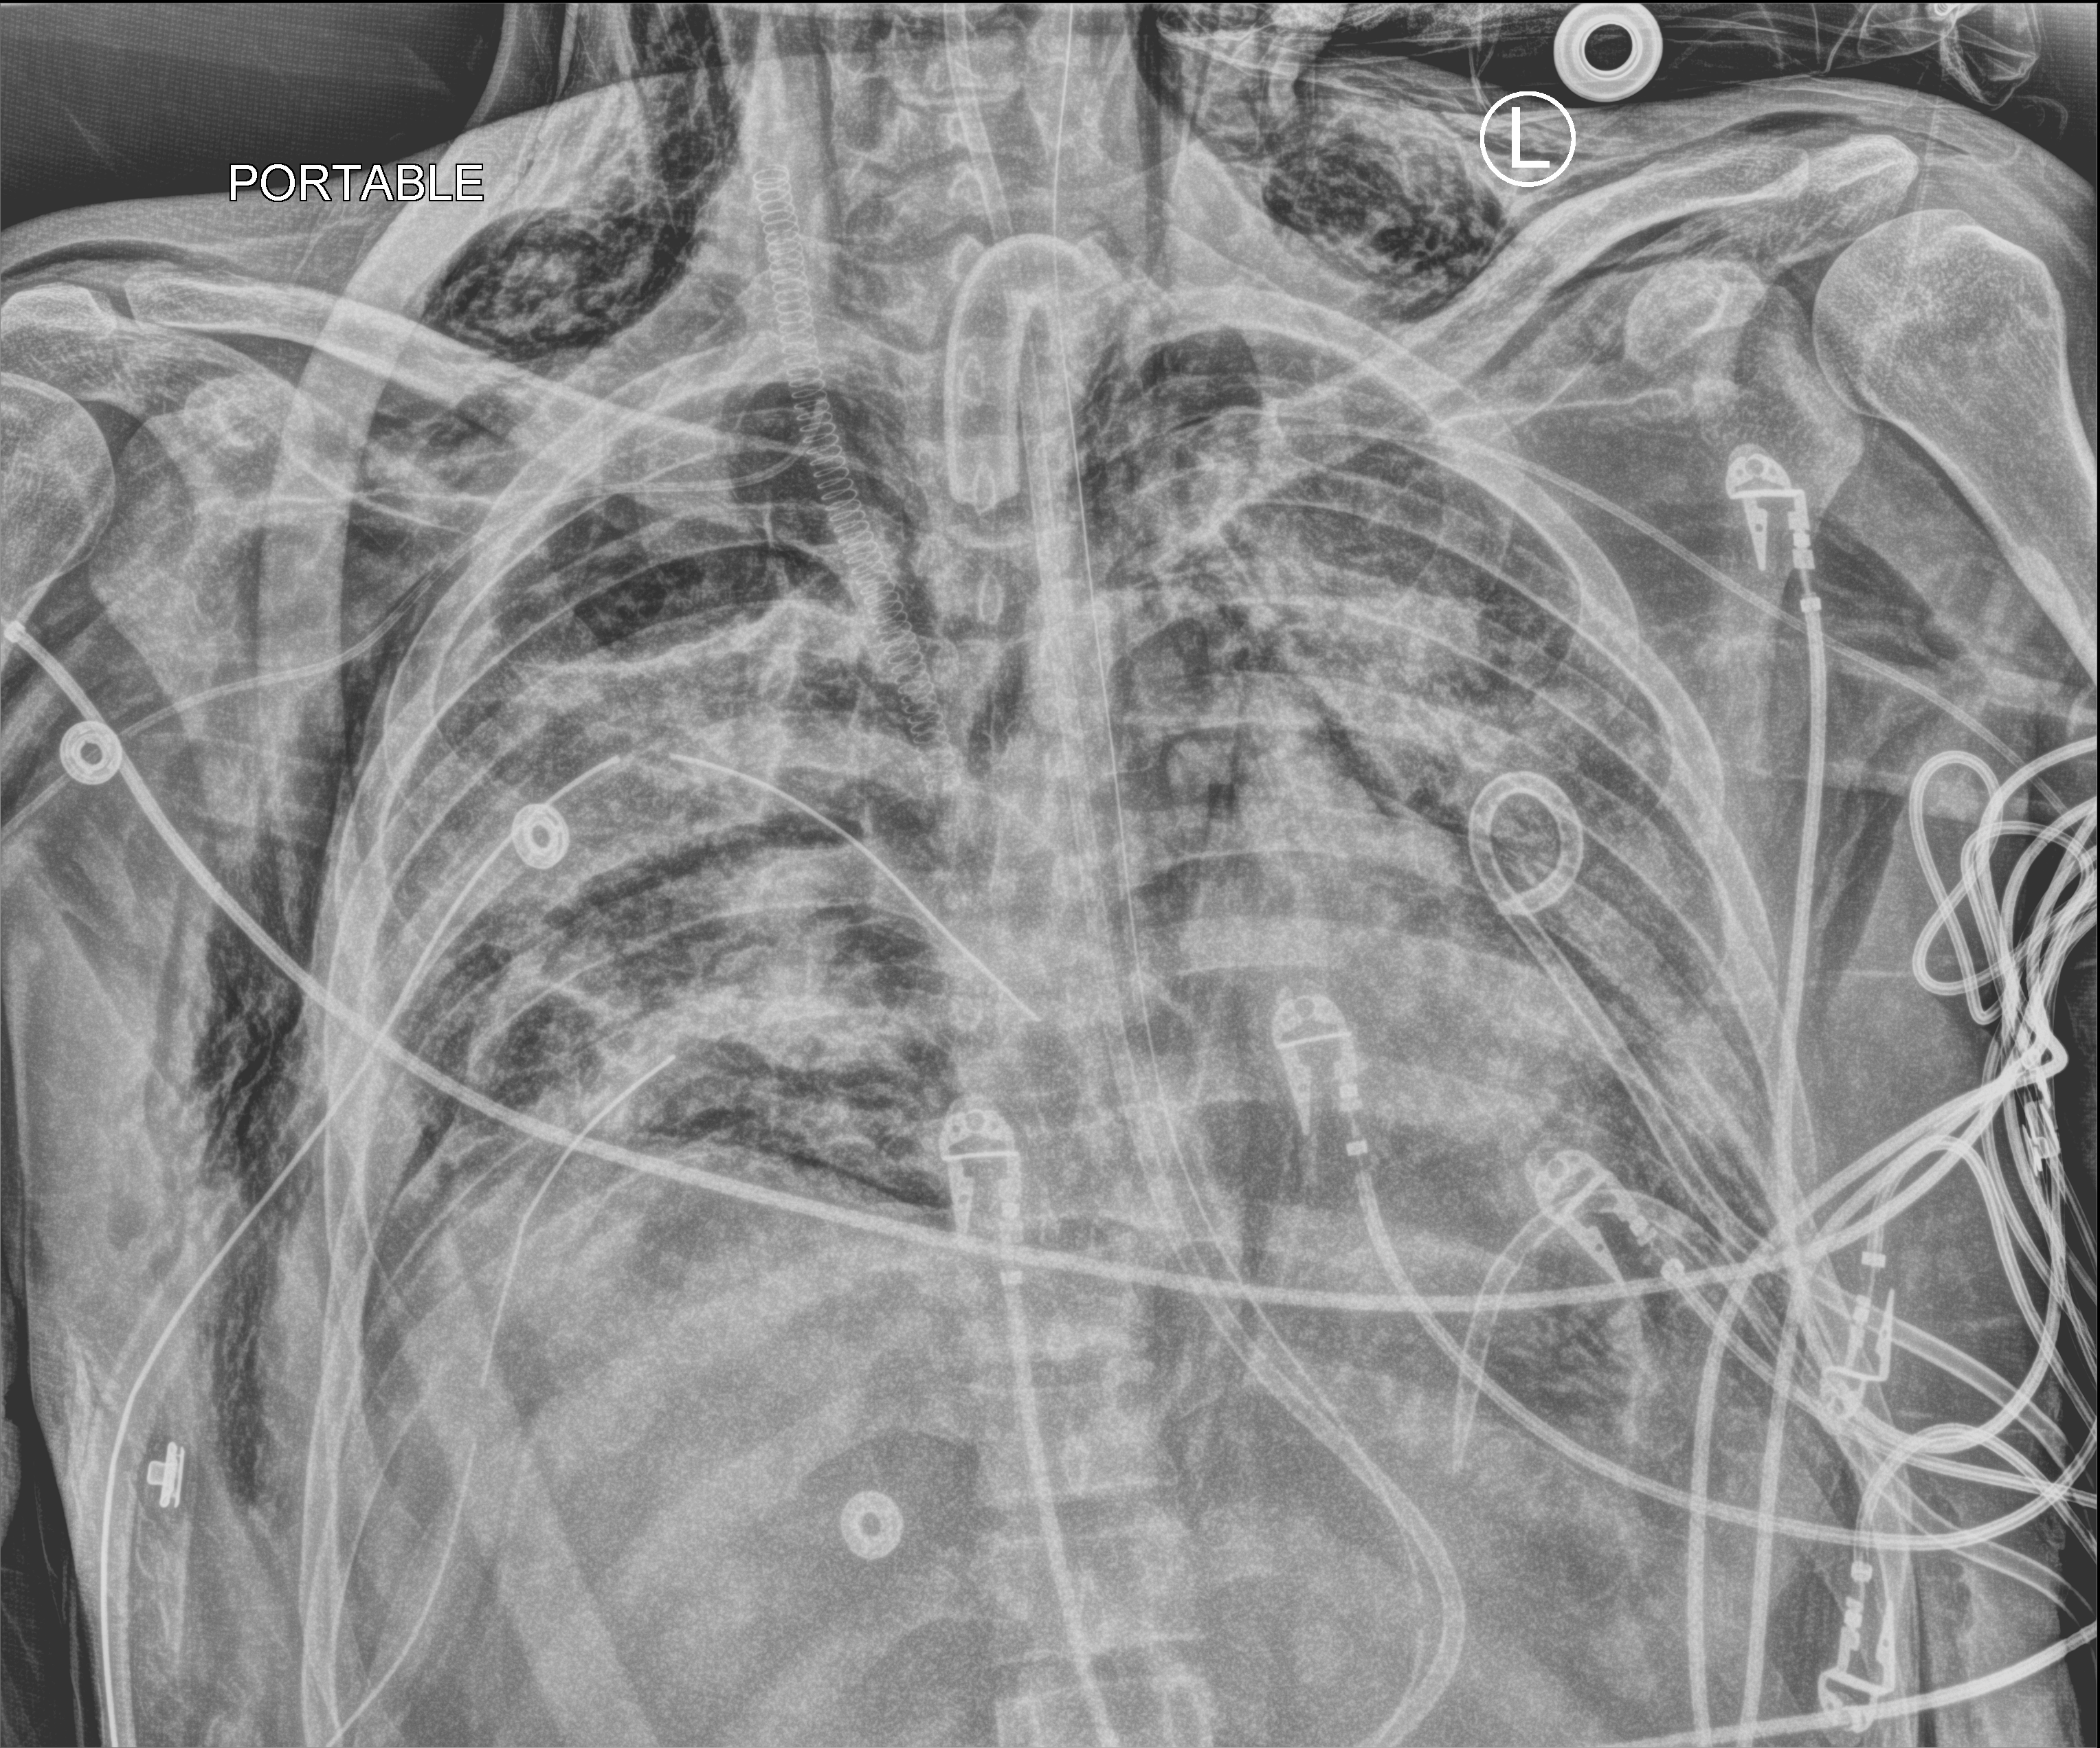
Bedside chest radiograph (computed radiography), anteroposterior (AP) projection. Patient hospitalised with COVID-19, aged 18–59 years.
Admission-level facts for this patient (not findings on this image; timing relative to this image not recorded): COPD (admission record): no; mechanically ventilated during this hospital stay: yes; admitted to intensive care during this hospital stay: yes.